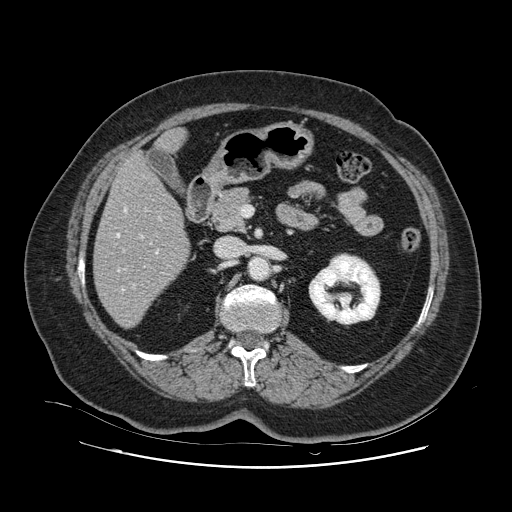
Contrast-enhanced abdominal CT, one axial slice. Slice 45 of 132 in the series (ordered by position). Soft-tissue window (W 400 / L 40 HU). 2.5 mm slice thickness. 512 × 512 image matrix, field of view 391 × 391 mm. Female patient, age 73 years. Case-level facts recorded for this patient, not image findings: diagnosis: colorectal cancer liver metastases, imaged before liver resection; multiple liver metastases: no; largest metastasis: 7 cm; disease in both lobes: no.
Outlined on this slice (outlined manually by an expert reader):
- hepatic veins: bounding box (x1, y1, x2, y2) in pixels: (116, 208, 159, 291)
- liver: (95, 131, 189, 327)
- planned liver remnant (the part of the liver to remain after resection): (95, 156, 189, 327)
- portal vein (with intrahepatic branches): (132, 217, 161, 289)